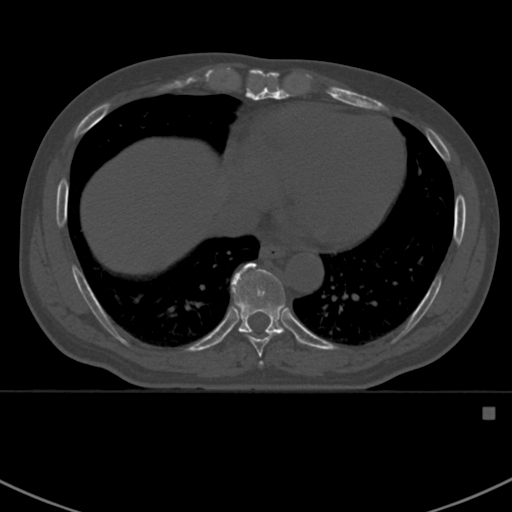
CT including the spine, one axial slice. Slice 391 of 412 in the series (ordered by position). Reconstruction kernel Br40s. 120 kVp. Bone window (W 1800 / L 400 HU). 1.5 mm slice thickness. 512 × 512 image matrix, field of view 358 × 358 mm. Patient: male, 59 years. From the clinical record (not read from this slice): primary cancer: prostate.
Annotated regions visible in this slice (semi-automatically segmented with operator editing):
- T7 vertebra: bounding box (x1, y1, x2, y2) in pixels: (259, 362, 263, 365)
- T8 vertebra: (245, 333, 280, 358)
- T9 vertebra: (232, 262, 285, 334)